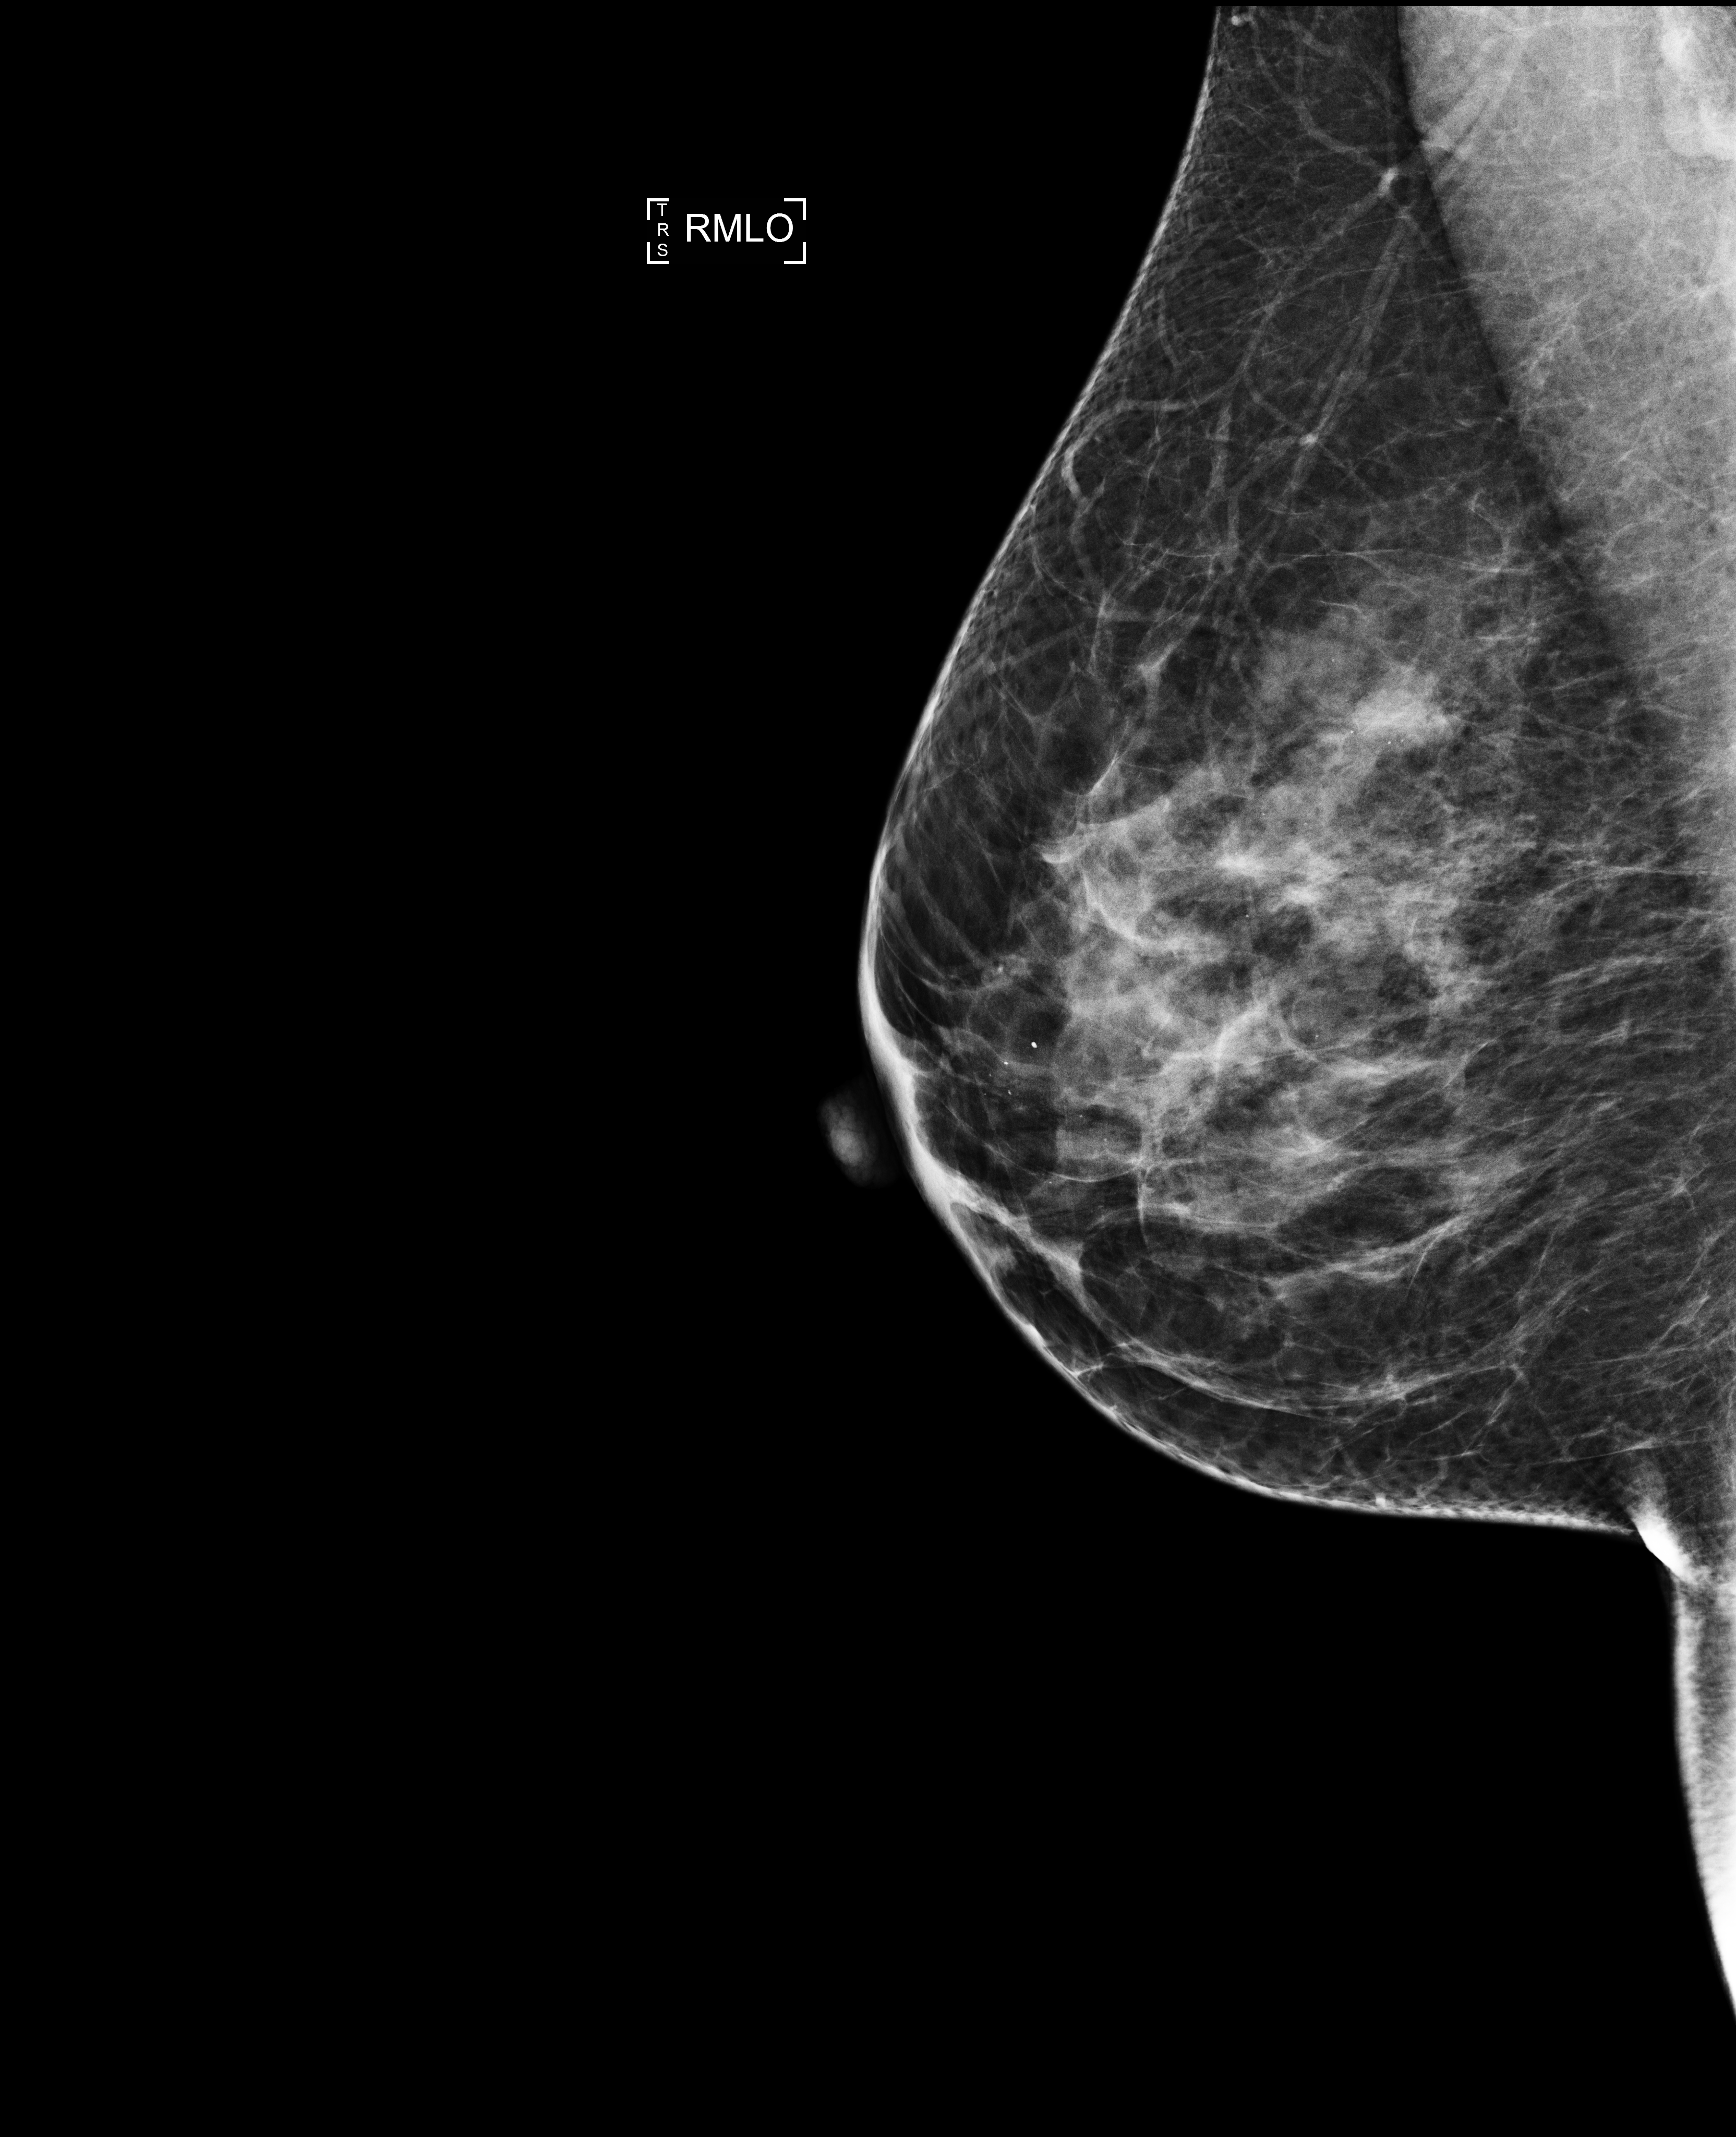
Annual screening mammography examination. Patient: female, 42 years.
Image type: full-field digital mammogram. Breast: right. Projection: medio-lateral oblique projection.